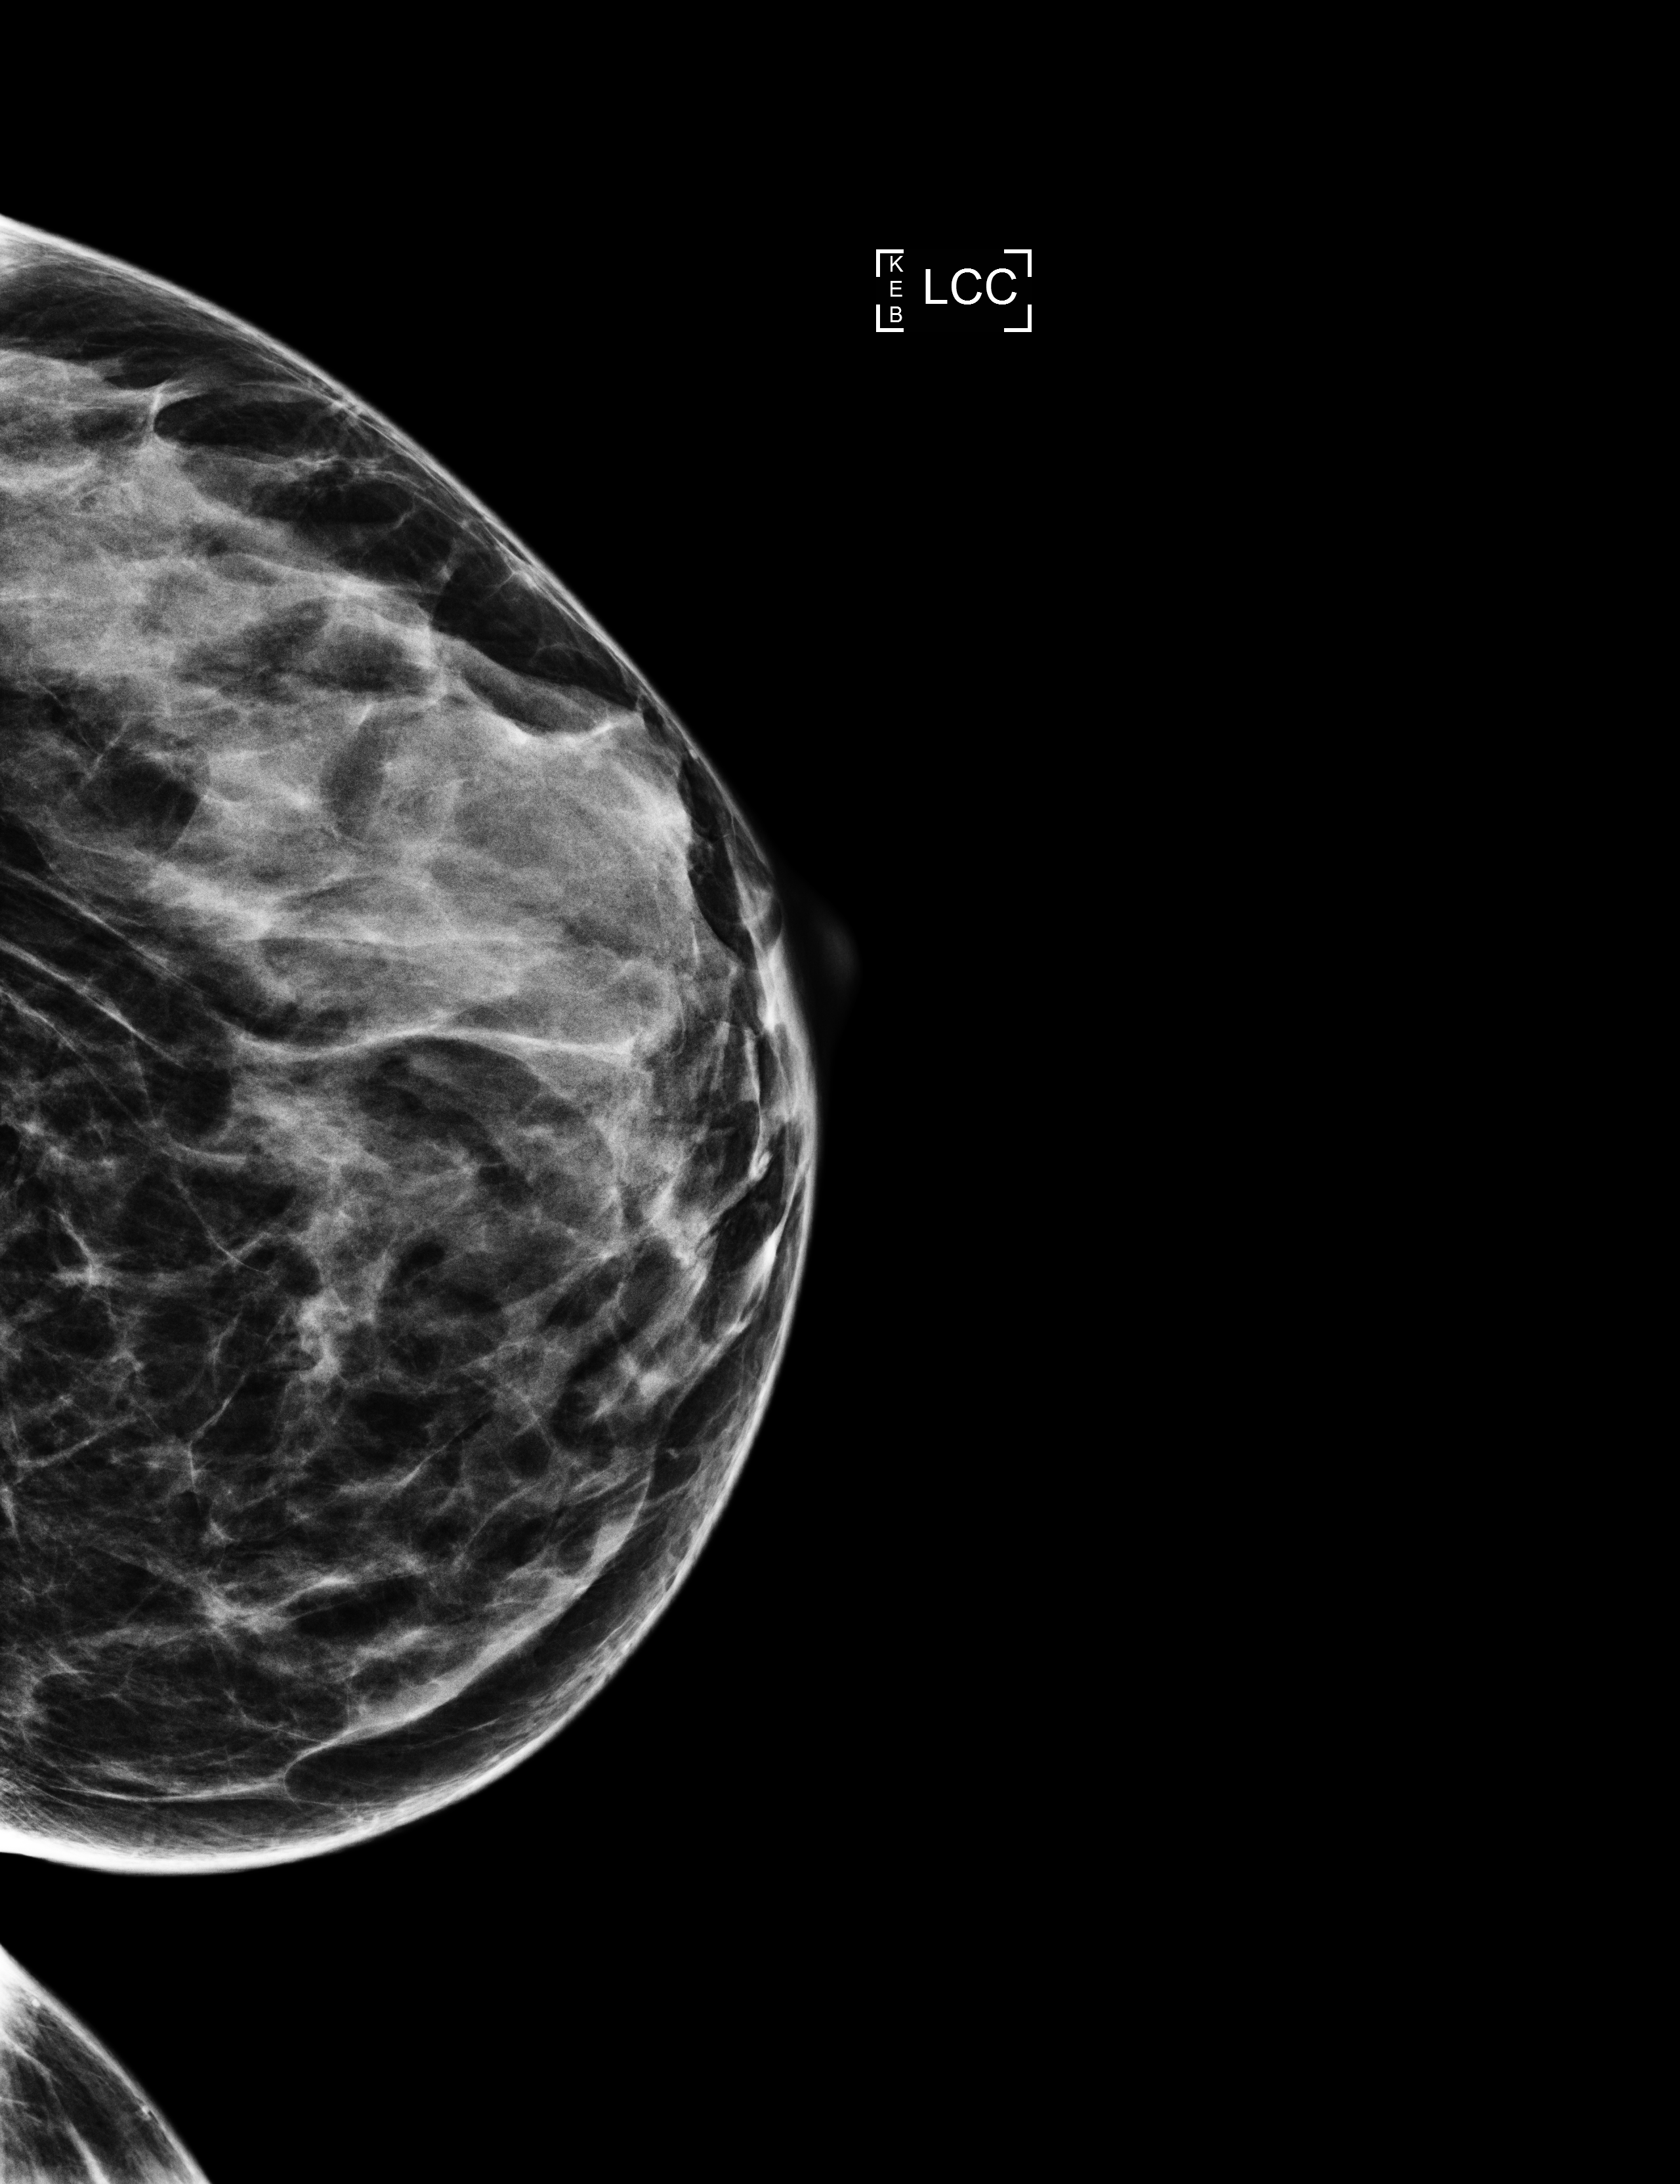
Diagnostic work-up study; compressed breast thickness 44 mm; system: Selenia Dimensions. Patient: female, 56 years.
Image type: full-field digital mammogram. Breast: left. Projection: cranio-caudal projection.